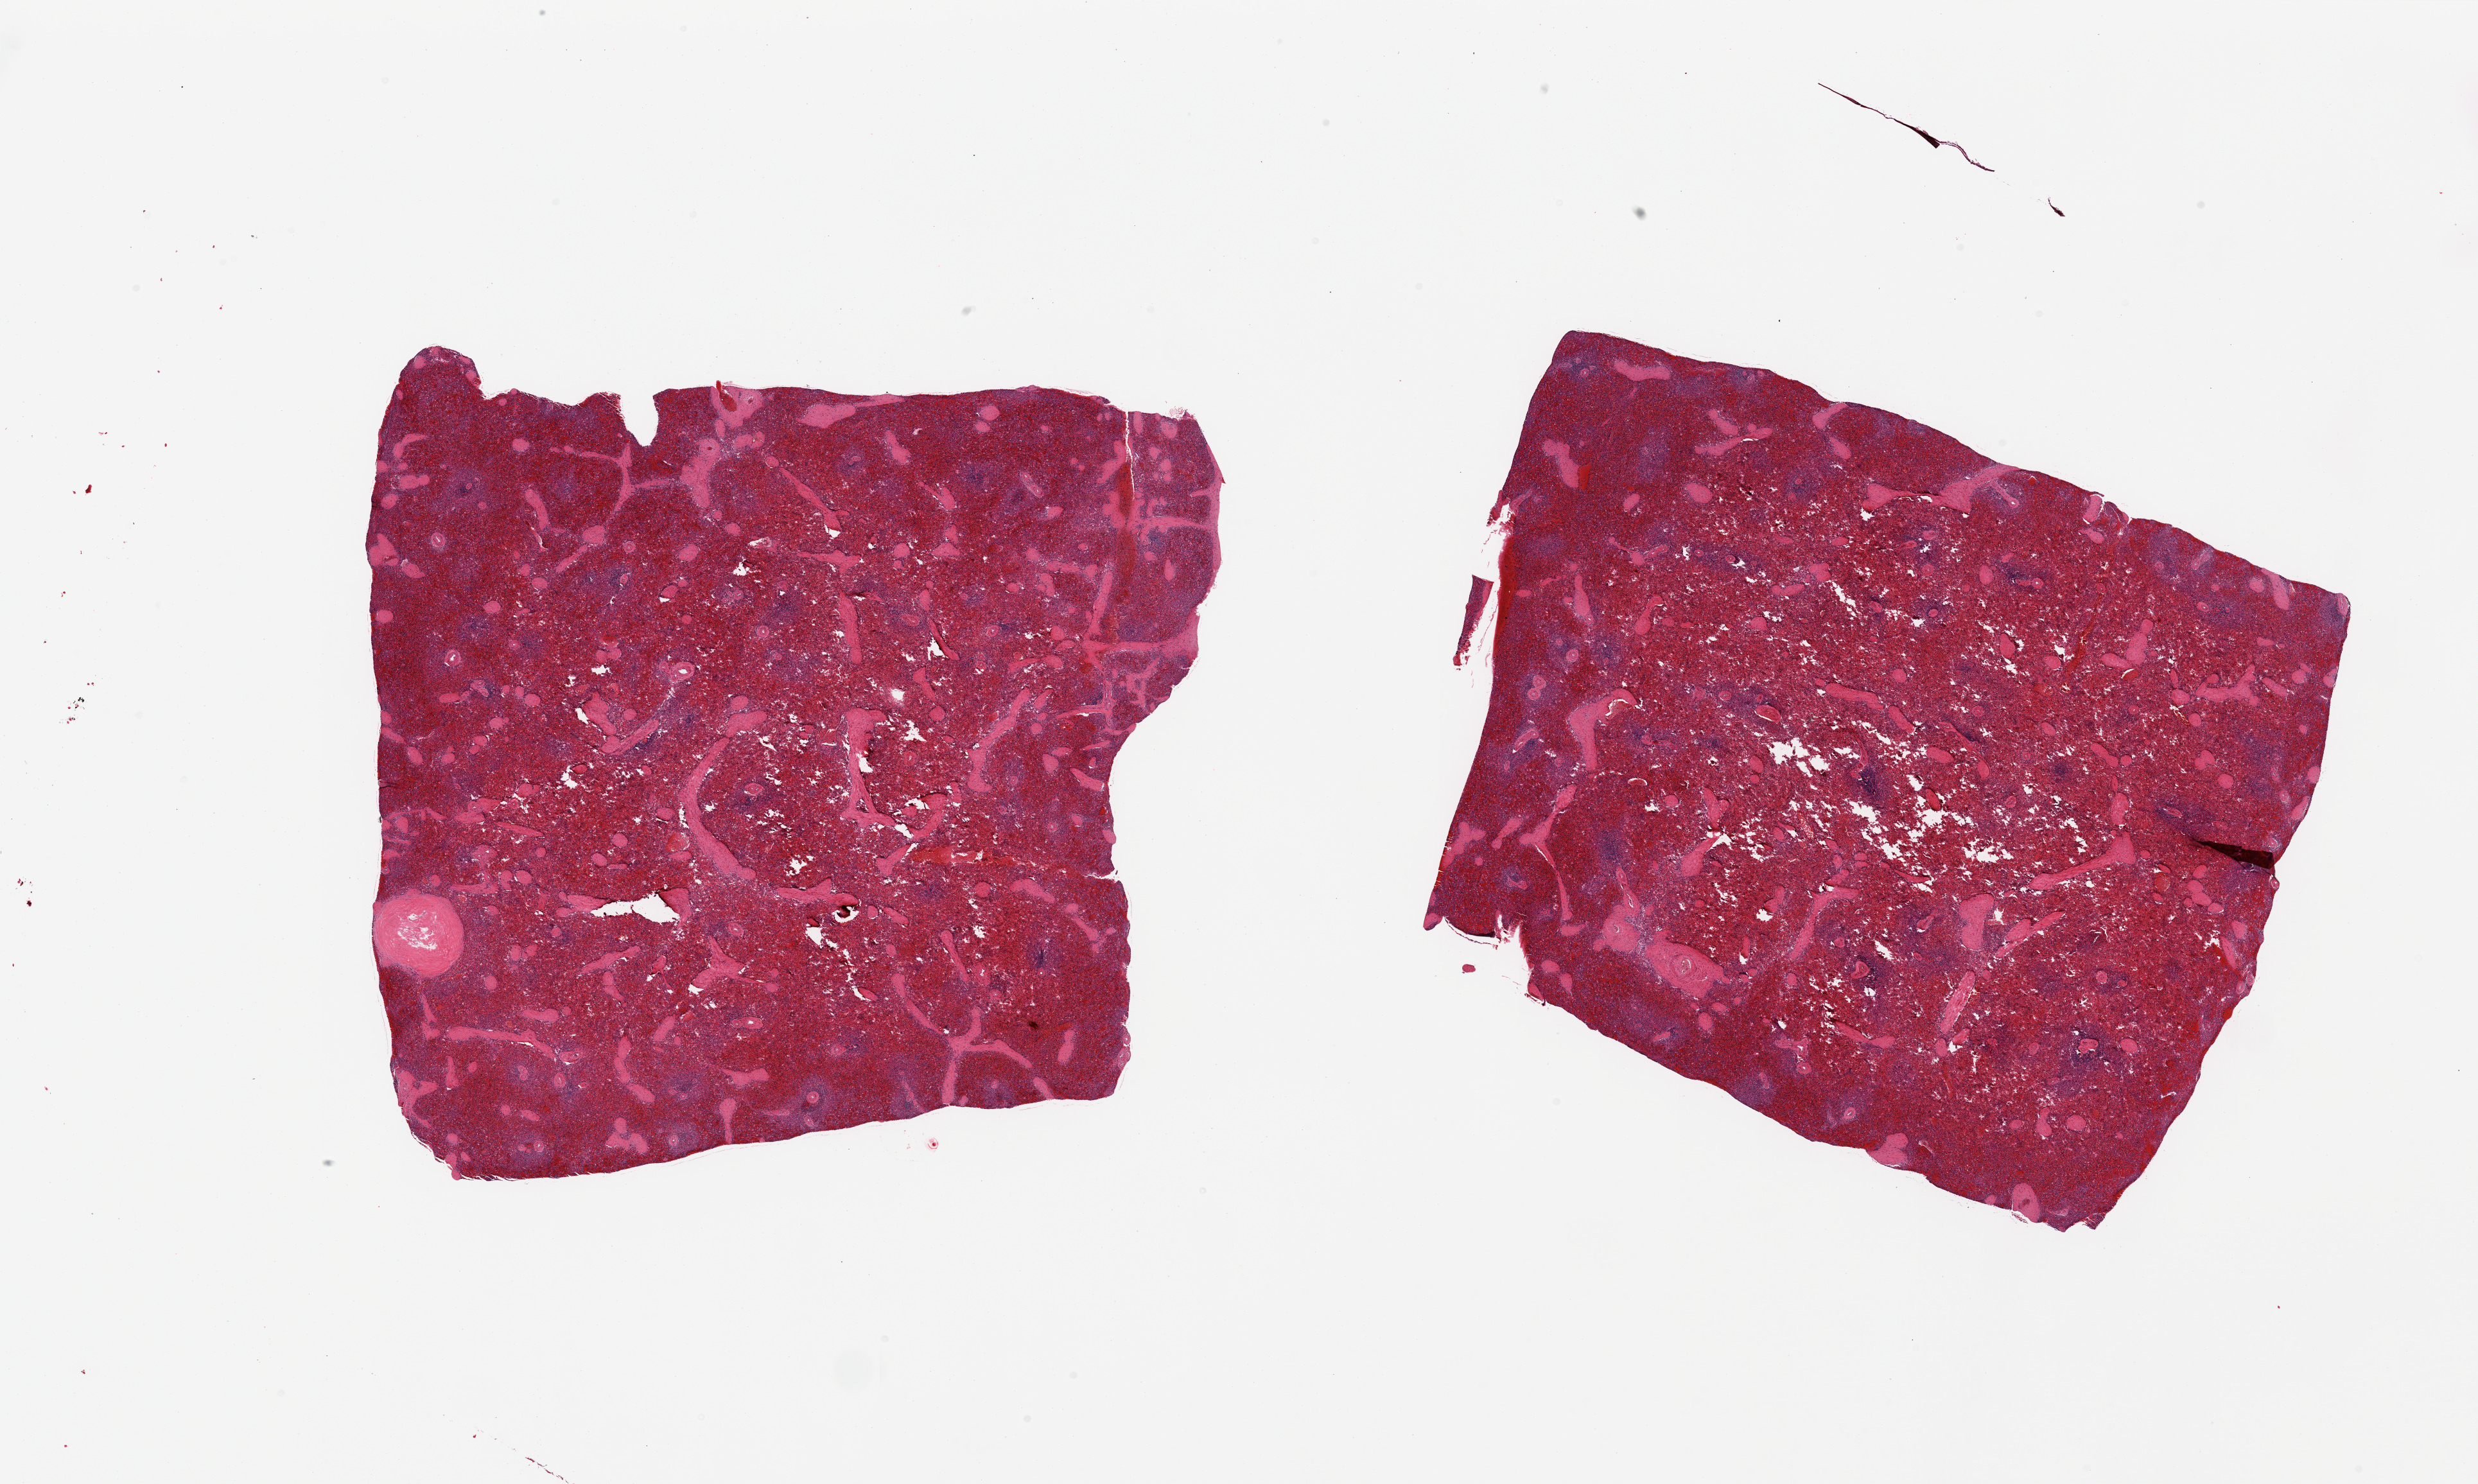
Whole-slide image, hematoxylin and eosin (H&E) stain — a low-resolution overview of the entire scanned area, about 30.5 x 18.3 mm; PAXgene-fixed paraffin-embedded (PFPE) section; target tissue: spleen; donor tissue sample. Donor sex: male.
Review note (as recorded): 2 pieces; congested.